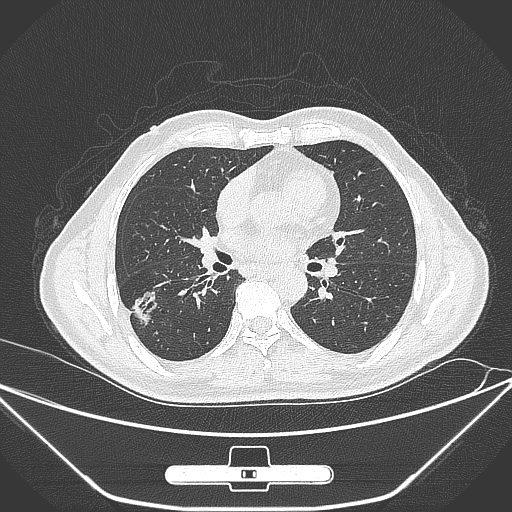
Chest CT, one axial slice; slice 147 of 310 in the series (ordered by position); 120 kVp; lung window (W 1500 / L -600 HU); 1 mm slice thickness; 512 × 512 image matrix. Male patient, age 71 years. Case-level facts recorded for this patient, not image findings: clinical TNM (as recorded): T1c N0 M0.
Annotated regions visible in this slice (bounding box drawn by a radiologist):
- lung tumour (recorded histology: adenocarcinoma): bounding box <130,287,160,336> (left, top, right, bottom; pixels)